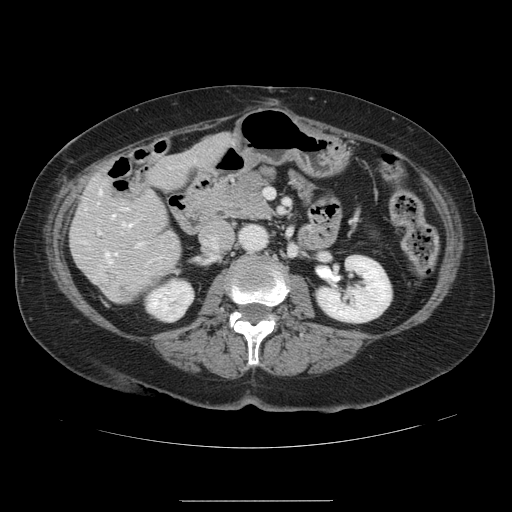
Contrast-enhanced abdominal CT, one axial slice; position 47 of 141 along the scan axis; 120 kVp; soft-tissue window (W 400 / L 40 HU); 512 × 512 image matrix. Female patient, age 74 years. From the clinical record (not read from this slice): diagnosis: colorectal cancer liver metastases, imaged before liver resection; multiple liver metastases: yes; largest metastasis: 7 cm; disease in both lobes: yes.
Structures marked on this image (outlined manually by an expert reader):
- hepatic veins: bounding box <98,190,131,263> (left, top, right, bottom; pixels)
- liver: <71,135,231,304>
- planned liver remnant (the part of the liver to remain after resection): <71,135,231,304>
- portal vein (with intrahepatic branches): <99,207,143,246>